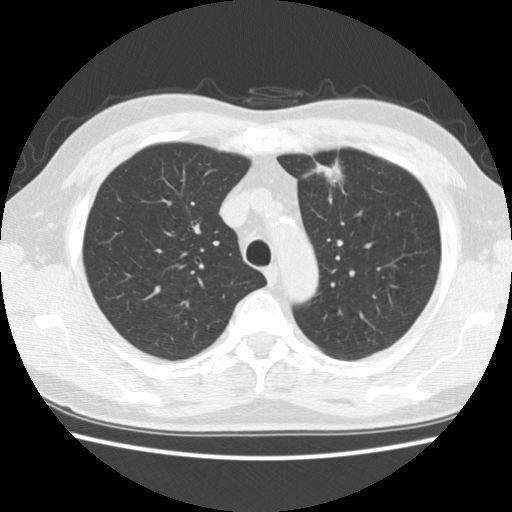
Low-dose screening chest CT, one axial slice. Position 129 of 172 along the scan axis. Lung window (W 1500 / L -600 HU). 2.5 mm slice thickness. 512 × 512 image matrix, field of view 337 × 337 mm.
Annotated regions visible in this slice (expert manual segmentation):
- lesion 1 (tumor, upper lobe of left lung): bounding box <312,159,343,184> (left, top, right, bottom; pixels)